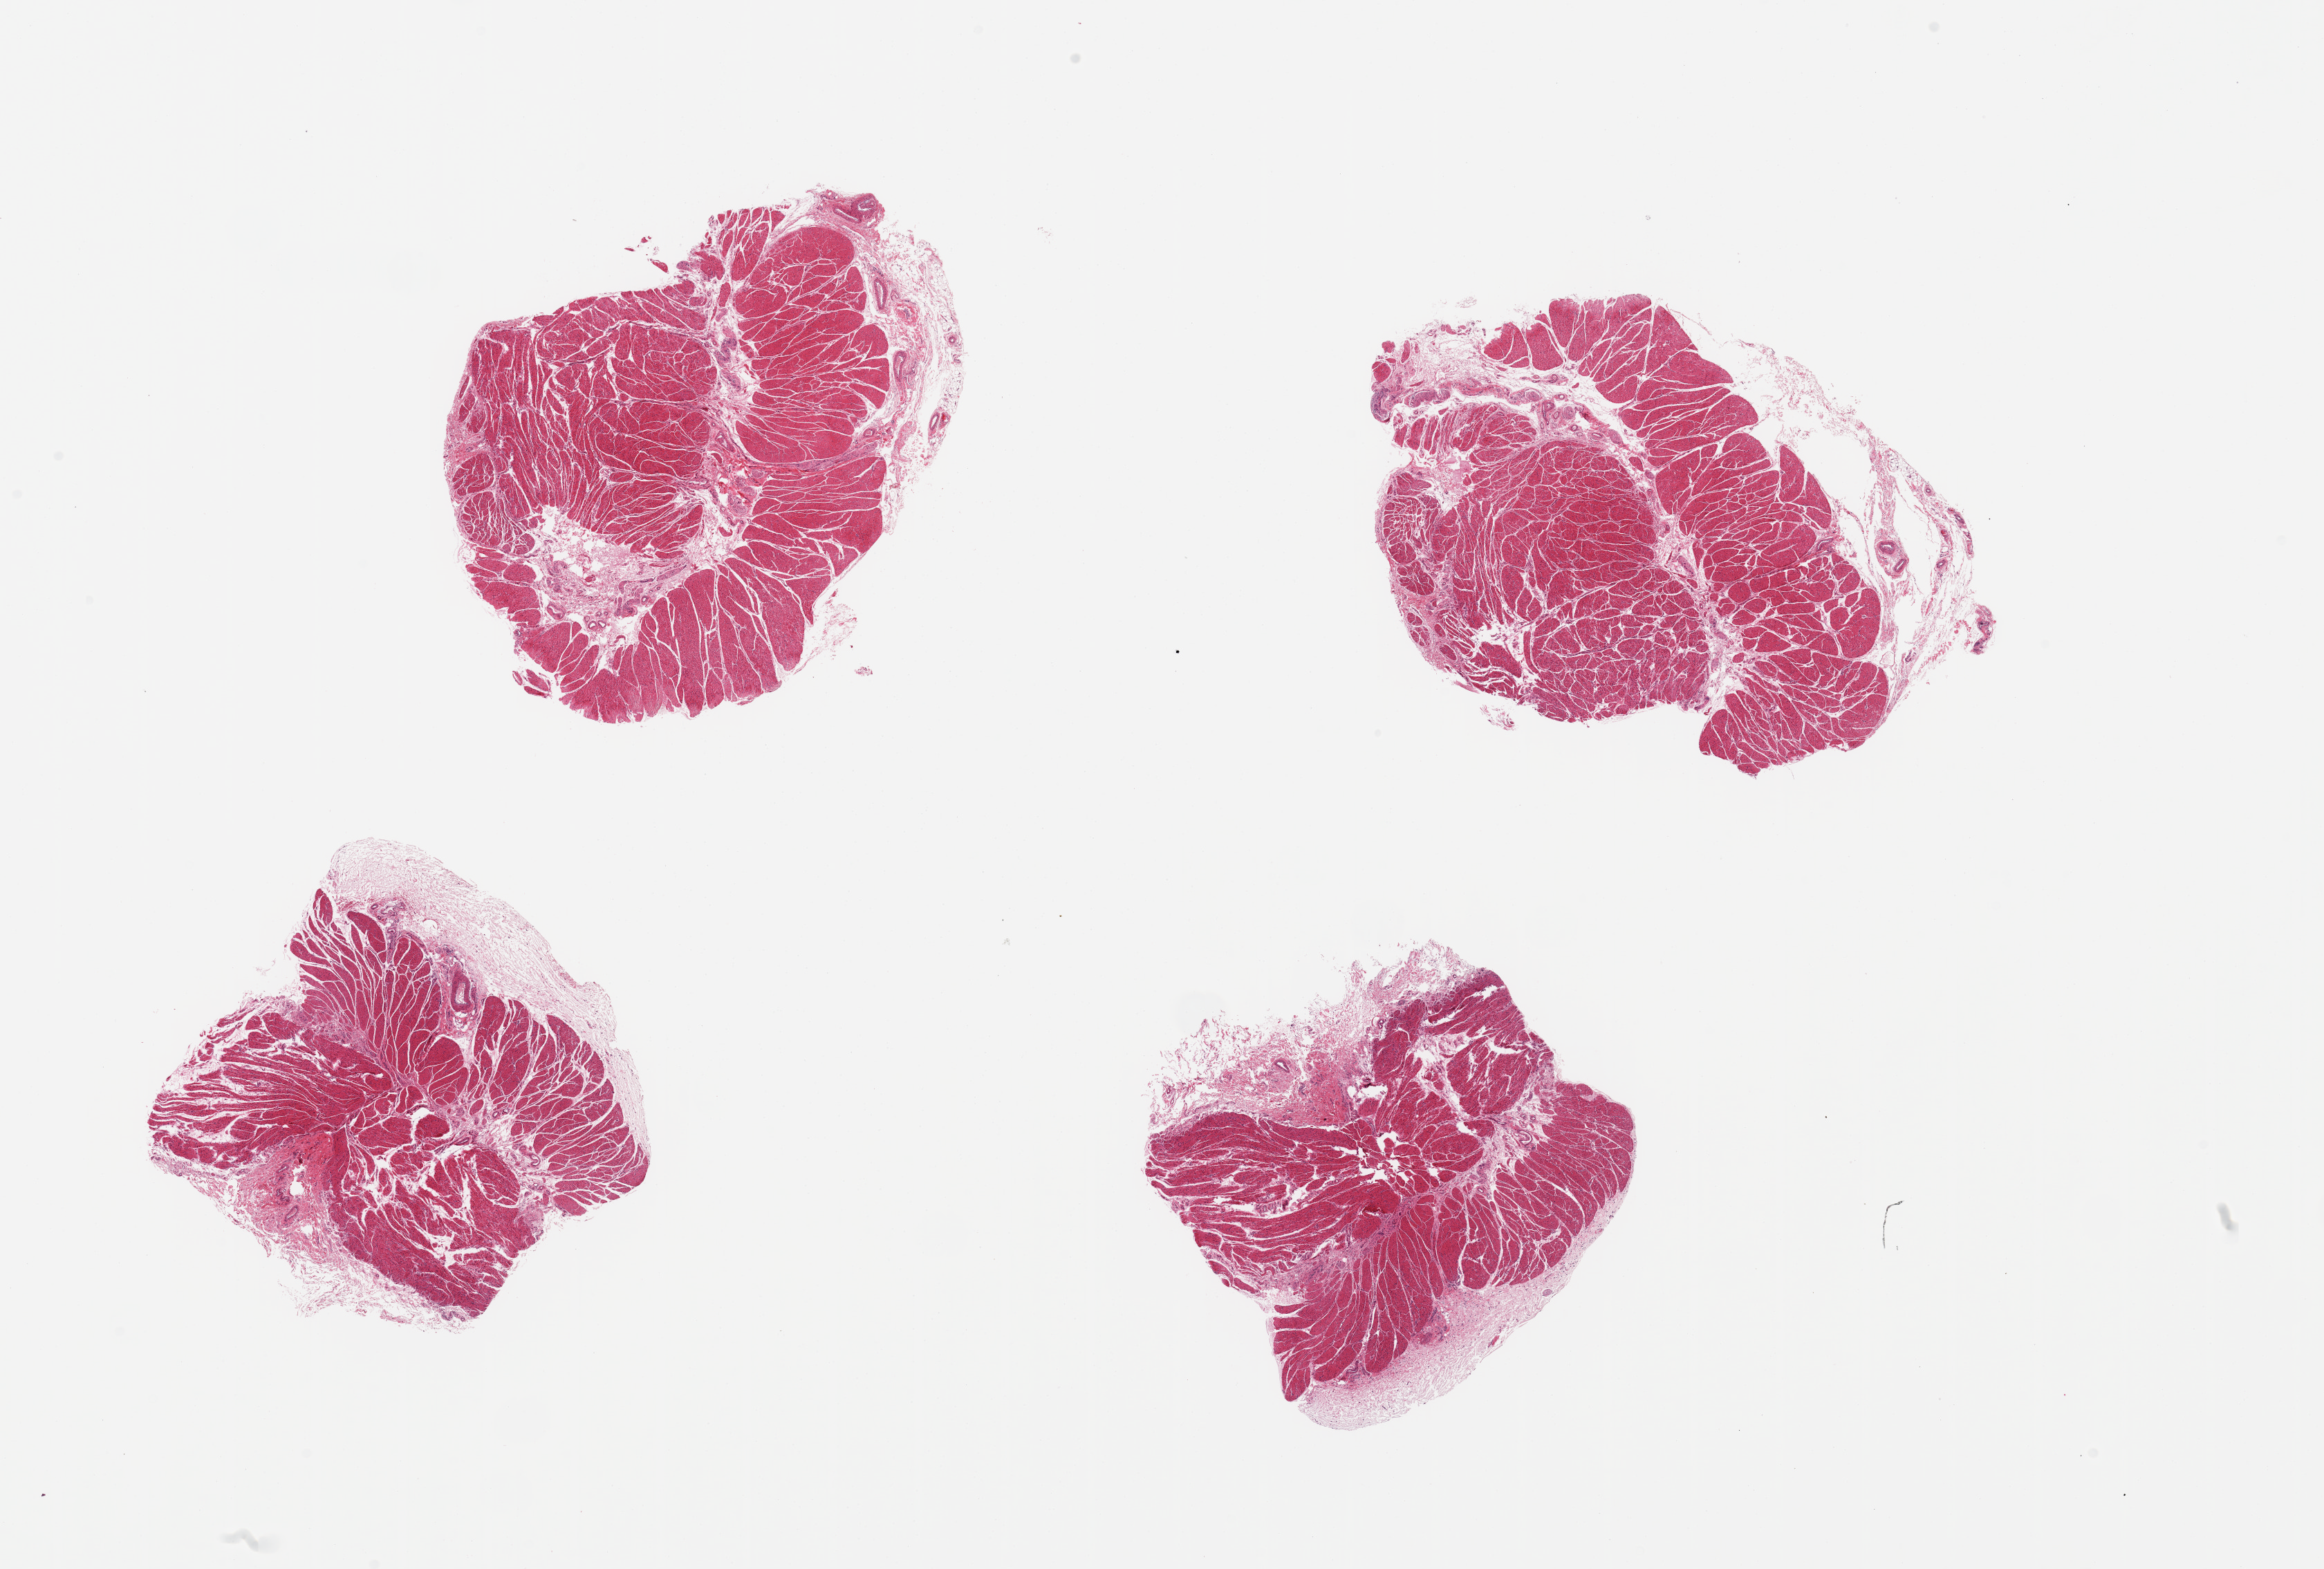
Hematoxylin and eosin (H&E) whole-slide image — whole scanned area (about 26.6 x 17.9 mm, acquisition: 20x scan) shown as a low-resolution overview. PAXgene-fixed, paraffin-embedded tissue. Section of esophageal muscle (target tissue). Tissue donor sample. Donor: male.
Pathologist's review note for this sample: 4 pieces, muscularis, adherent fat/serosa up to ~1mm, good specimens.